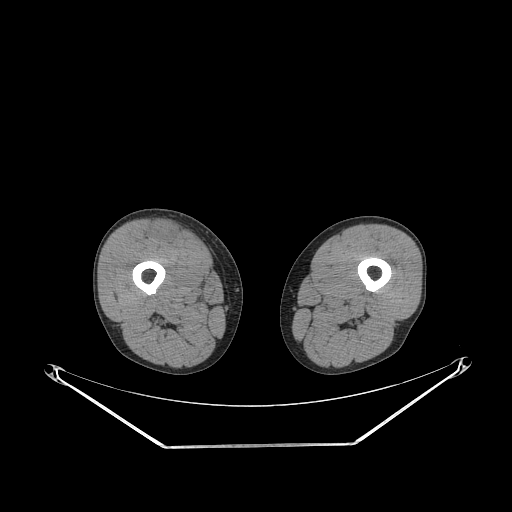
CT of an extremity soft-tissue mass (from a PET/CT study), one axial slice; position 239 of 311 along the scan axis; reconstruction kernel STANDARD; 140 kVp; soft-tissue window (W 400 / L 40 HU); 3.75 mm slice thickness; 512 × 512 image matrix, field of view 500 × 500 mm. Male patient. From the clinical record (not read from this slice): histological type: pleiomorphic leiomyosarcoma; grade: intermediate; site of the primary tumour: right thigh.
Outlined on this slice (expert contour drawn on MRI and transferred to this co-registered scan by the dataset authors):
- gross tumour volume including surrounding oedema: bounding box (x1, y1, x2, y2) in pixels: (153, 222, 181, 243)